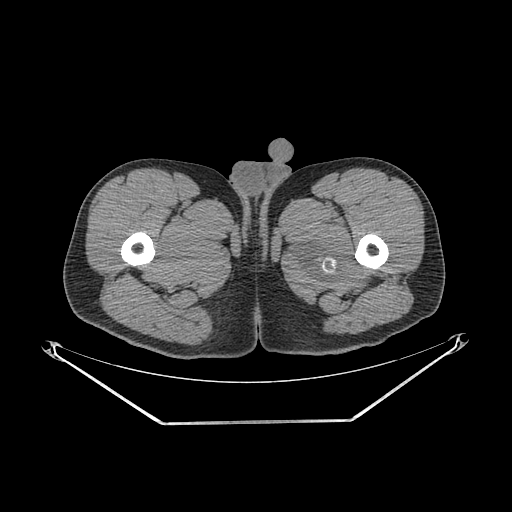
CT of an extremity soft-tissue mass (from a PET/CT study), one axial slice. Slice 261 of 267 in the series (ordered by position). Reconstruction kernel SOFT. Soft-tissue window (W 400 / L 40 HU). 512 × 512 image matrix, field of view 500 × 500 mm. Male patient. Case-level facts recorded for this patient, not image findings: histological type: extraskeletal osteosarcoma; grade: high; site of the primary tumour: left adductur.
Annotated regions visible in this slice (expert contour drawn on MRI and transferred to this co-registered scan by the dataset authors):
- gross tumour volume (mass): bounding box [x1, y1, x2, y2] px = [286, 206, 385, 300]